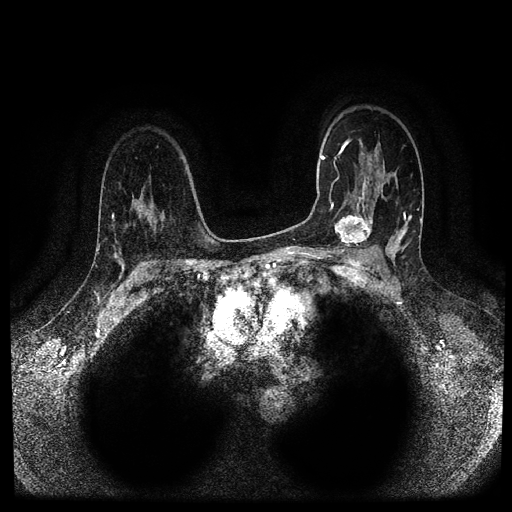
Breast MRI (dynamic contrast-enhanced, multi-phase), one axial slice. Slice 70 of 116 in the series (ordered by position). Dynamic contrast-enhanced series, time point 2 of 5 at this slice position (early post-contrast). 1.5 T. TE 2.6 ms, TR 5.3 ms. 2 mm slice thickness. 512 × 512 image matrix, field of view 350 × 350 mm. Female patient, age 44 years.
Structures marked on this image (semi-automatic segmentation, software-assisted and operator-edited):
- breast lesion (labelled 'tumour' in the annotation; benign lesions carry a separate 'benign' label): bounding box [x1, y1, x2, y2] px = [334, 208, 374, 251]